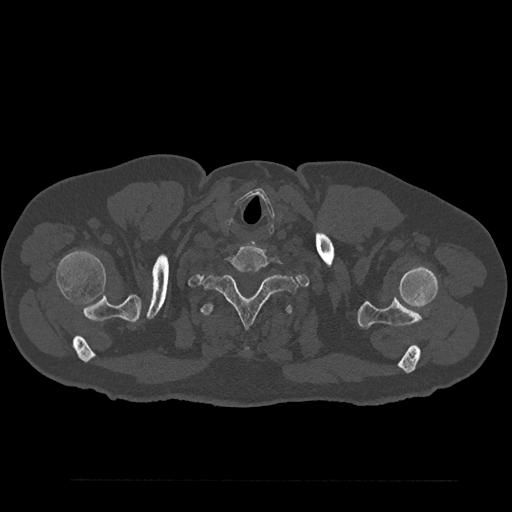
CT including the spine, one axial slice. Slice 754 of 797 in the series (ordered by position). Reconstruction kernel Br40s/3. Bone window (W 1800 / L 400 HU). 512 × 512 image matrix. Patient: male, 61 years. From the clinical record (not read from this slice): primary cancer: prostate.
Structures marked on this image (semi-automatically segmented with operator editing):
- T1 vertebra: box from (x=203, y=274) to (x=298, y=326) px
- T2 vertebra: (x=200, y=301)–(x=294, y=352)